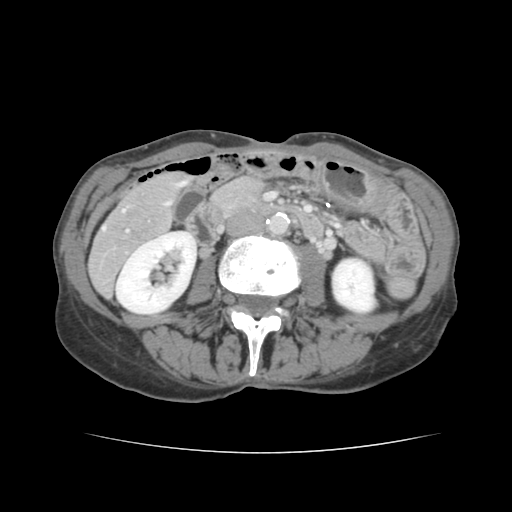
Contrast-enhanced abdominal CT, one axial slice; slice 40 of 136 in the series (ordered by position); 120 kVp; intravenous contrast given; soft-tissue window (W 400 / L 40 HU); 512 × 512 image matrix. Female patient, age 77 years. Case-level facts recorded for this patient, not image findings: diagnosis: colorectal cancer liver metastases, imaged before liver resection; multiple liver metastases: yes; largest metastasis: 3 cm; disease in both lobes: no.
Outlined on this slice (expert manual segmentation):
- hepatic veins: bounding box [x1, y1, x2, y2] px = [103, 202, 169, 230]
- liver: [89, 174, 184, 293]